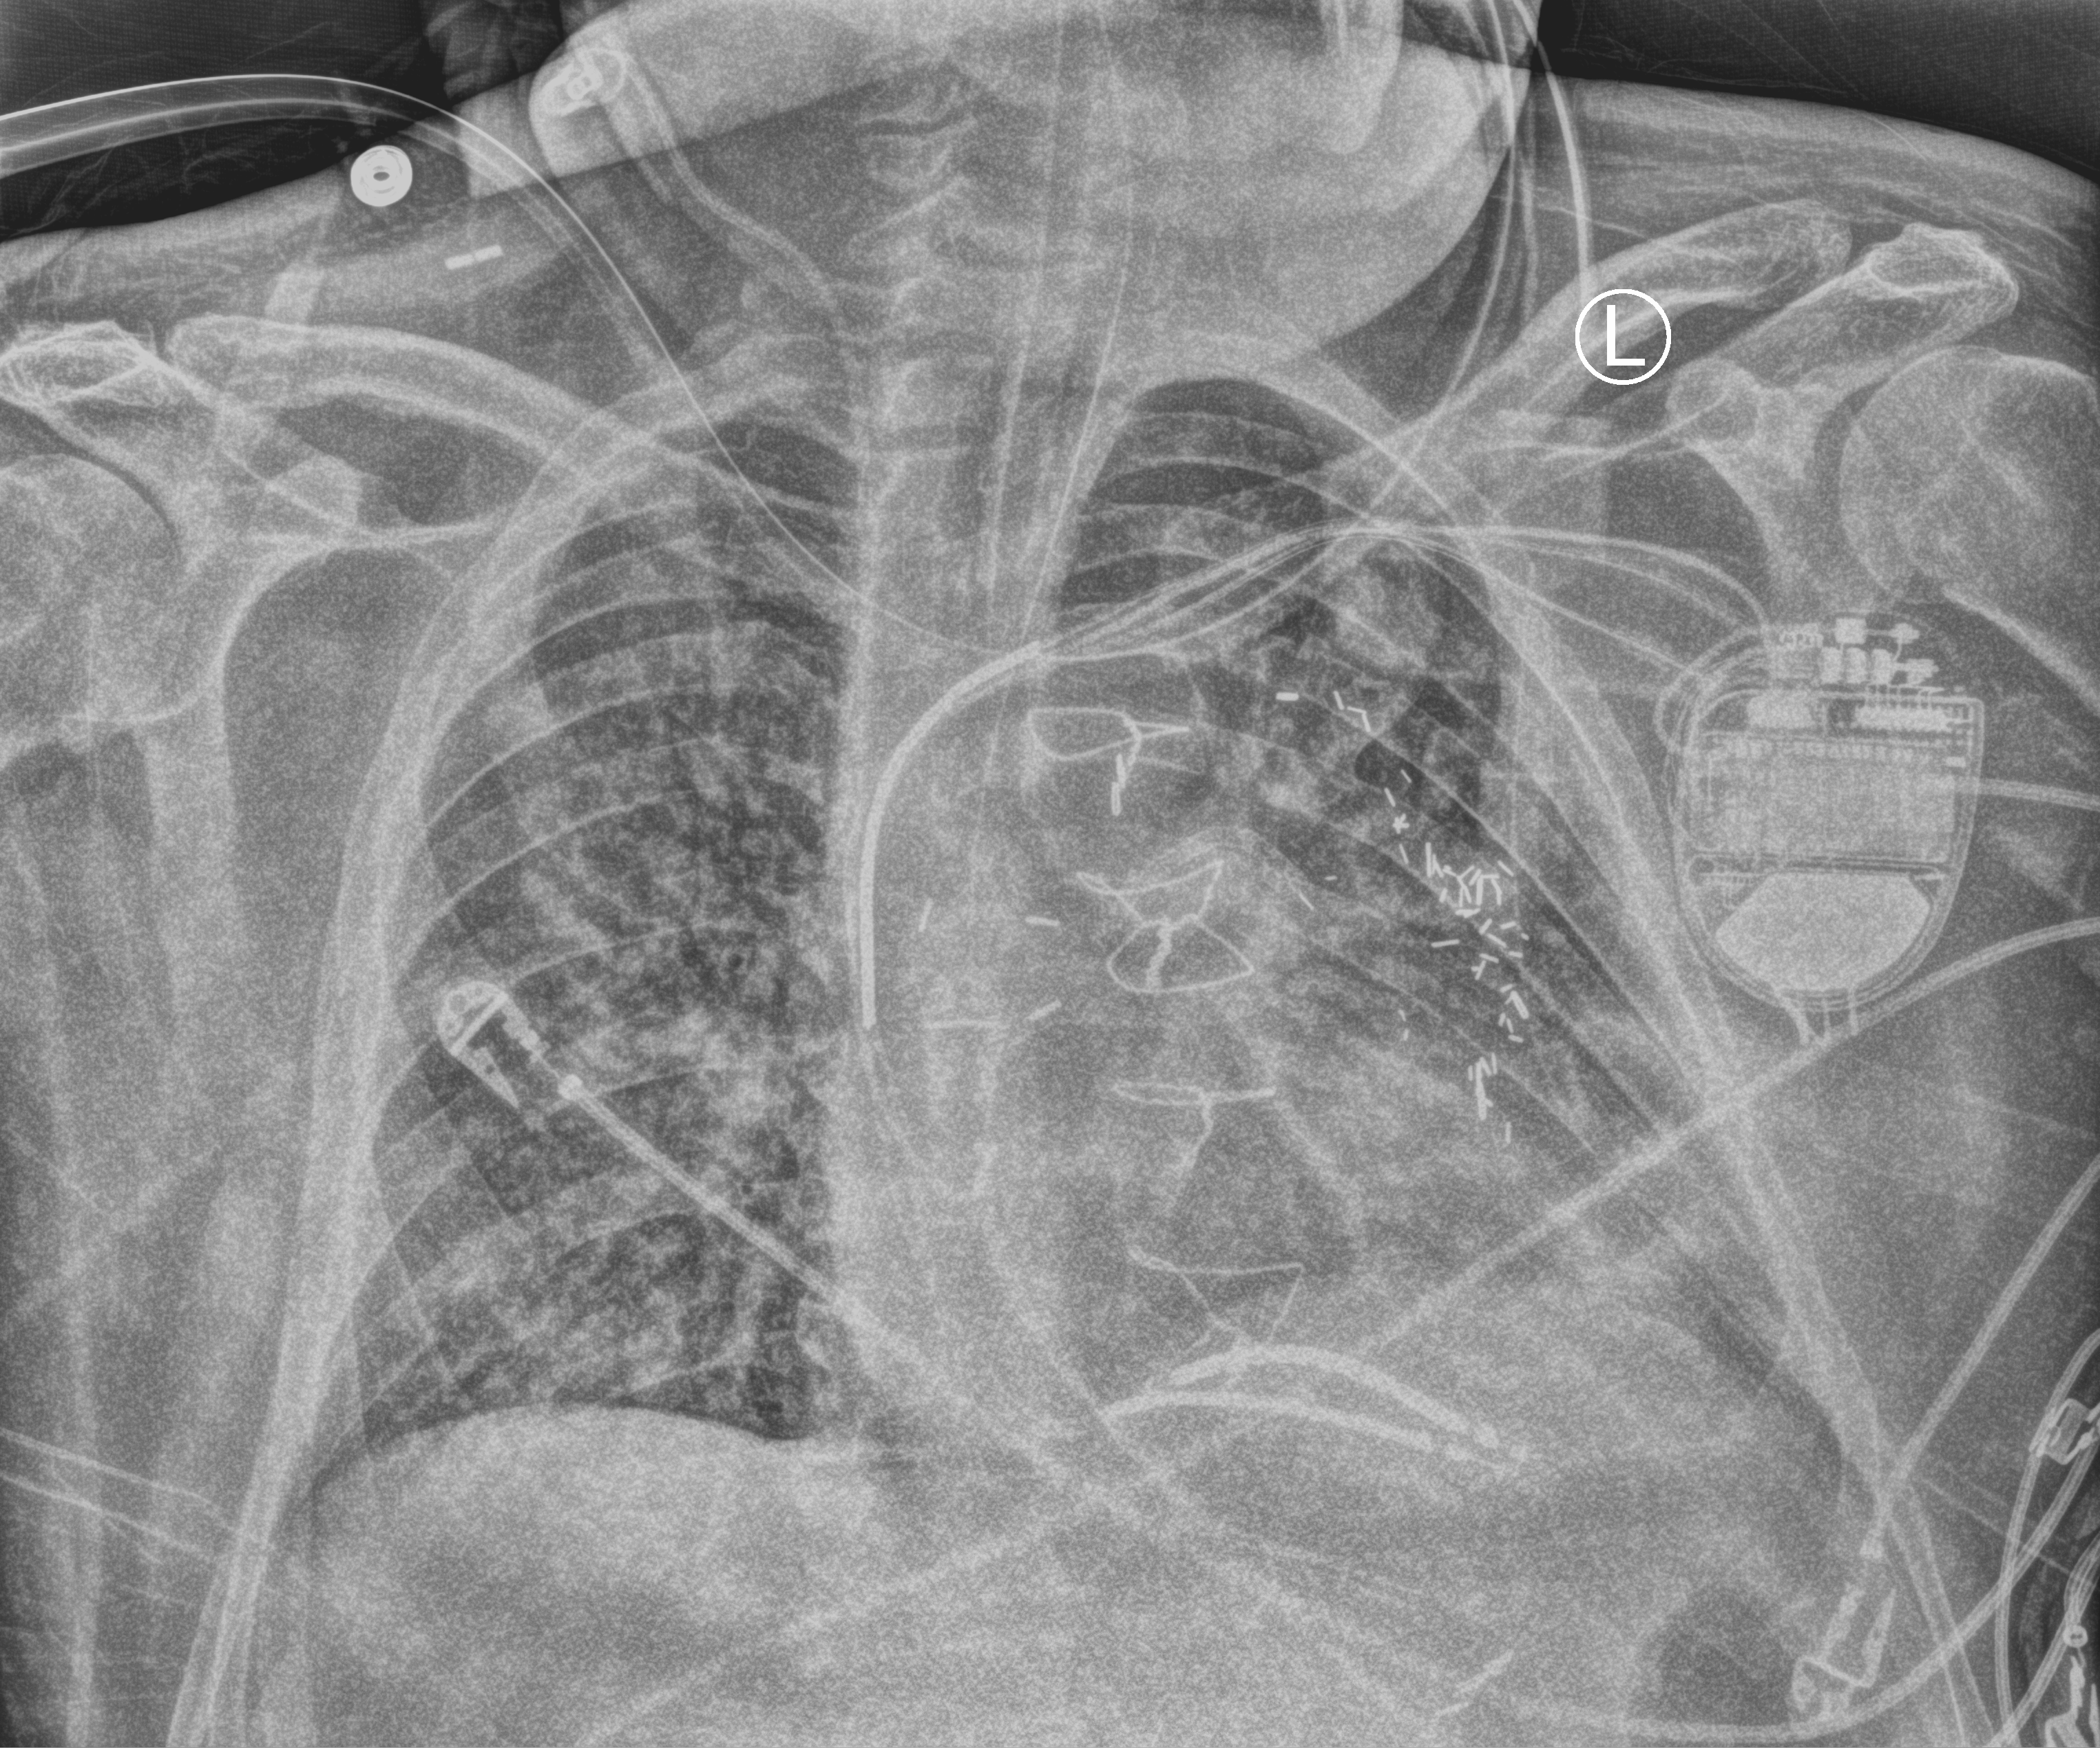
Chest X-ray (portable), anteroposterior (AP) projection. Patient hospitalised with COVID-19; male, aged 60–74 years.
Admission-level facts for this patient (not findings on this image; timing relative to this image not recorded): mechanically ventilated during this hospital stay: yes; admitted to intensive care during this hospital stay: yes.